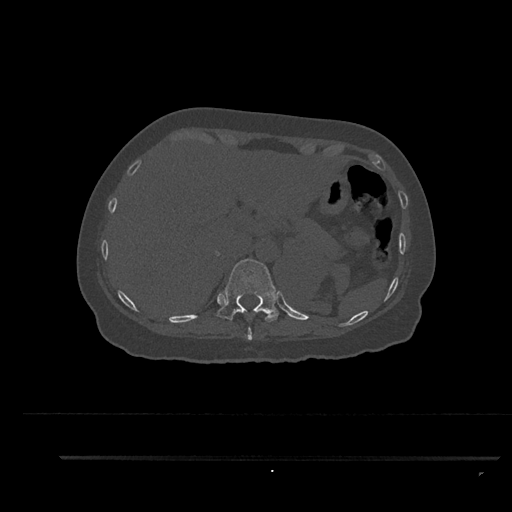
CT including the spine, one axial slice. Position 327 of 797 along the scan axis. 120 kVp. Bone window (W 1800 / L 400 HU). 512 × 512 image matrix, field of view 408 × 408 mm. Female patient, age 44 years. From the clinical record (not read from this slice): primary cancer: renal; vertebrae with lytic lesions (as recorded): L1.
Outlined on this slice (semi-automatically segmented with operator editing):
- T10 vertebra: bounding box (x1, y1, x2, y2) in pixels: (244, 311, 253, 340)
- T11 vertebra: (216, 259, 279, 322)